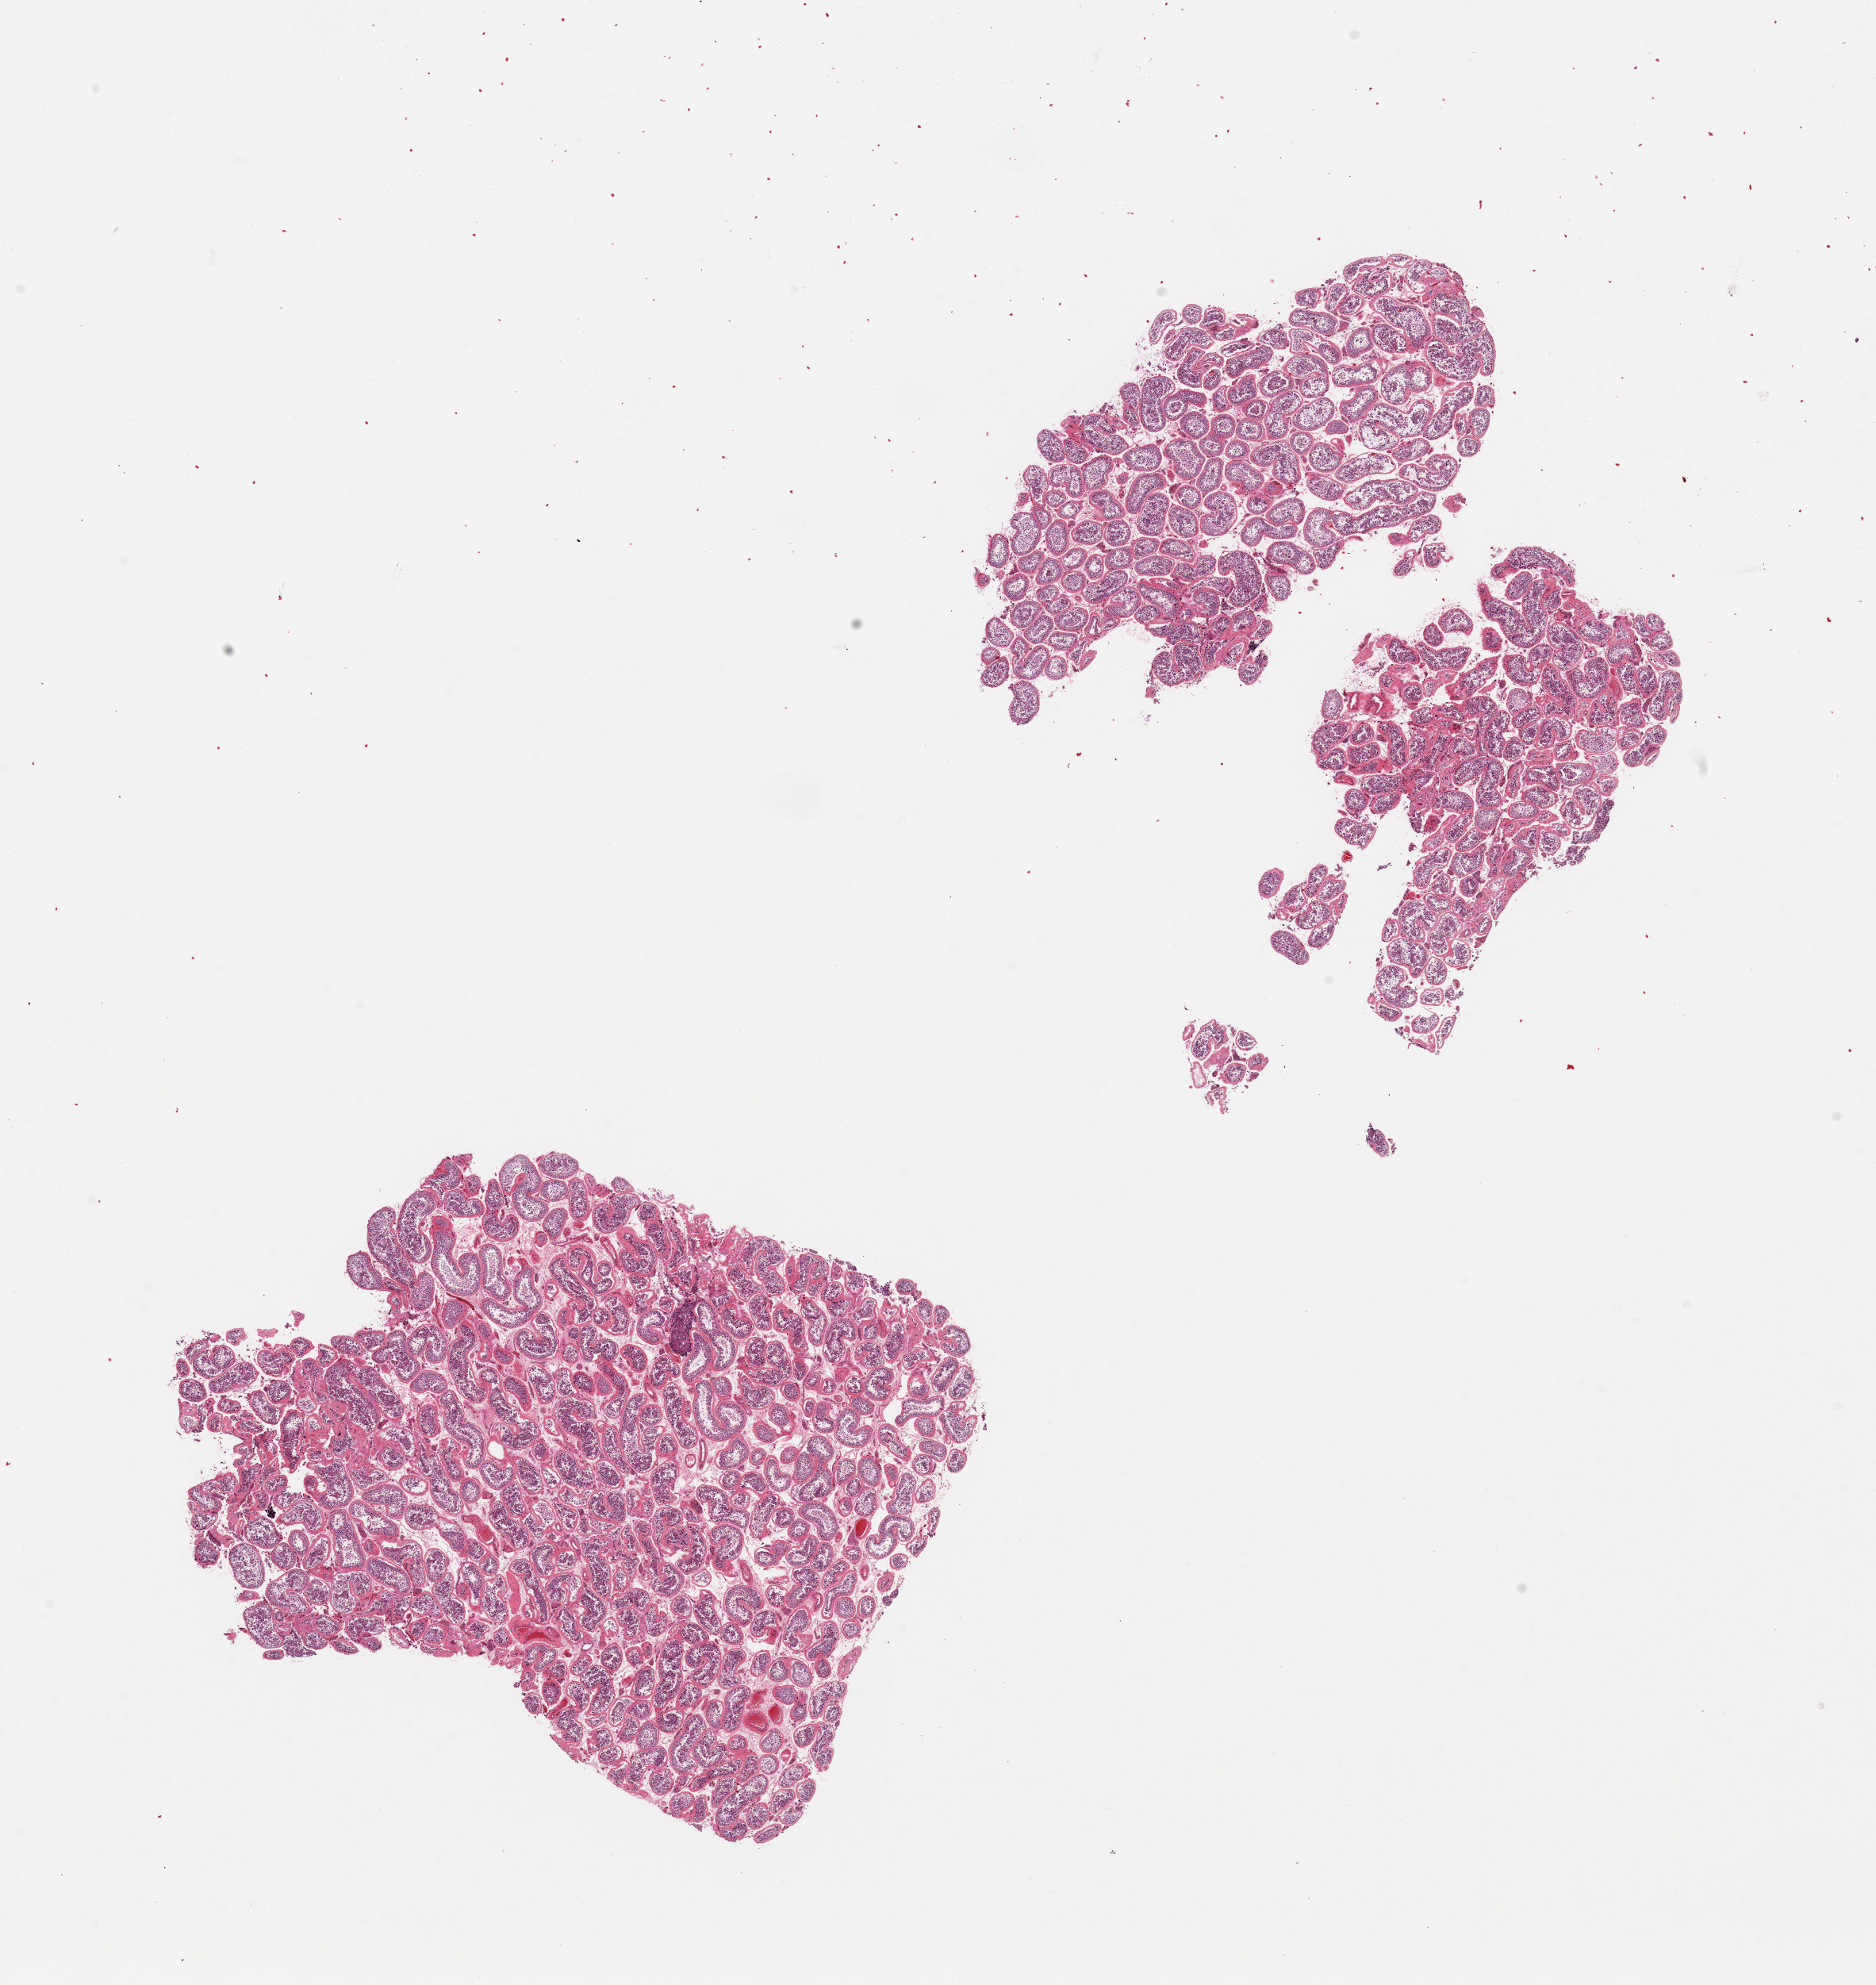
H&E whole-slide image, a low-resolution overview of the entire scanned area, about 18.7 x 19.8 mm (slide scanned at 20x); PAXgene-fixed, paraffin-embedded tissue; target tissue: testis; donor tissue sample. Donor: male.
- review note (as recorded): 2 pieces, spermatogenesis appears reduced